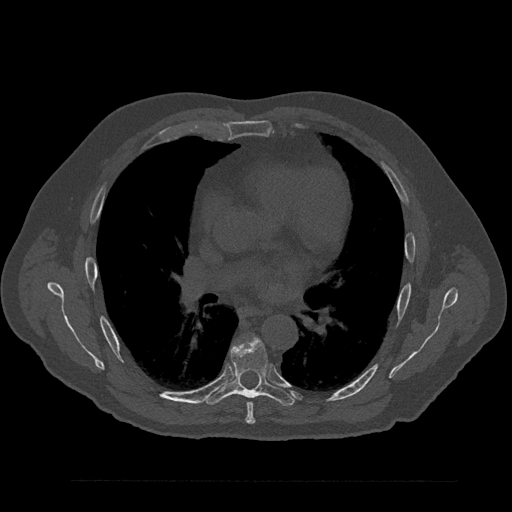
CT including the spine, one axial slice. Slice 522 of 797 in the series (ordered by position). Reconstruction kernel Br40s/3. Bone window (W 1800 / L 400 HU). 0.5 mm slice thickness. 512 × 512 image matrix. Patient: male, 61 years. From the clinical record (not read from this slice): primary cancer: prostate.
Outlined on this slice (semi-automatic segmentation, software-assisted and operator-edited):
- T6 vertebra: bounding box <246,402,256,424> (left, top, right, bottom; pixels)
- T7 vertebra: <204,336,295,406>